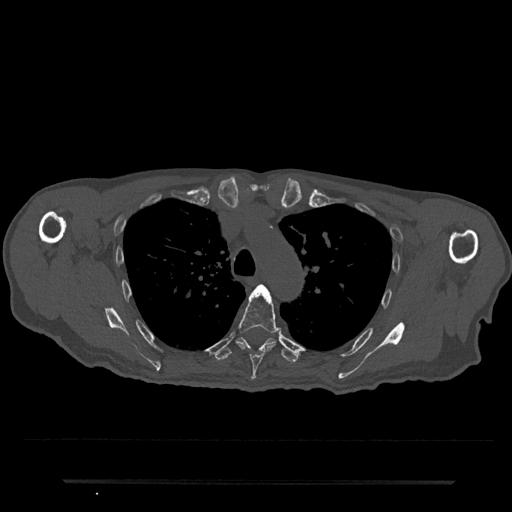
CT including the spine, one axial slice. Slice 565 of 797 in the series (ordered by position). Reconstruction kernel Br40s/3. Bone window (W 1800 / L 400 HU). 0.5 mm slice thickness. 512 × 512 image matrix, field of view 427 × 427 mm. Patient: male, 74 years. From the clinical record (not read from this slice): primary cancer: prostate.
Outlined on this slice (semi-automatic segmentation, software-assisted and operator-edited):
- T5 vertebra: bounding box [x1, y1, x2, y2] px = [238, 285, 282, 380]
- T6 vertebra: [214, 337, 299, 363]